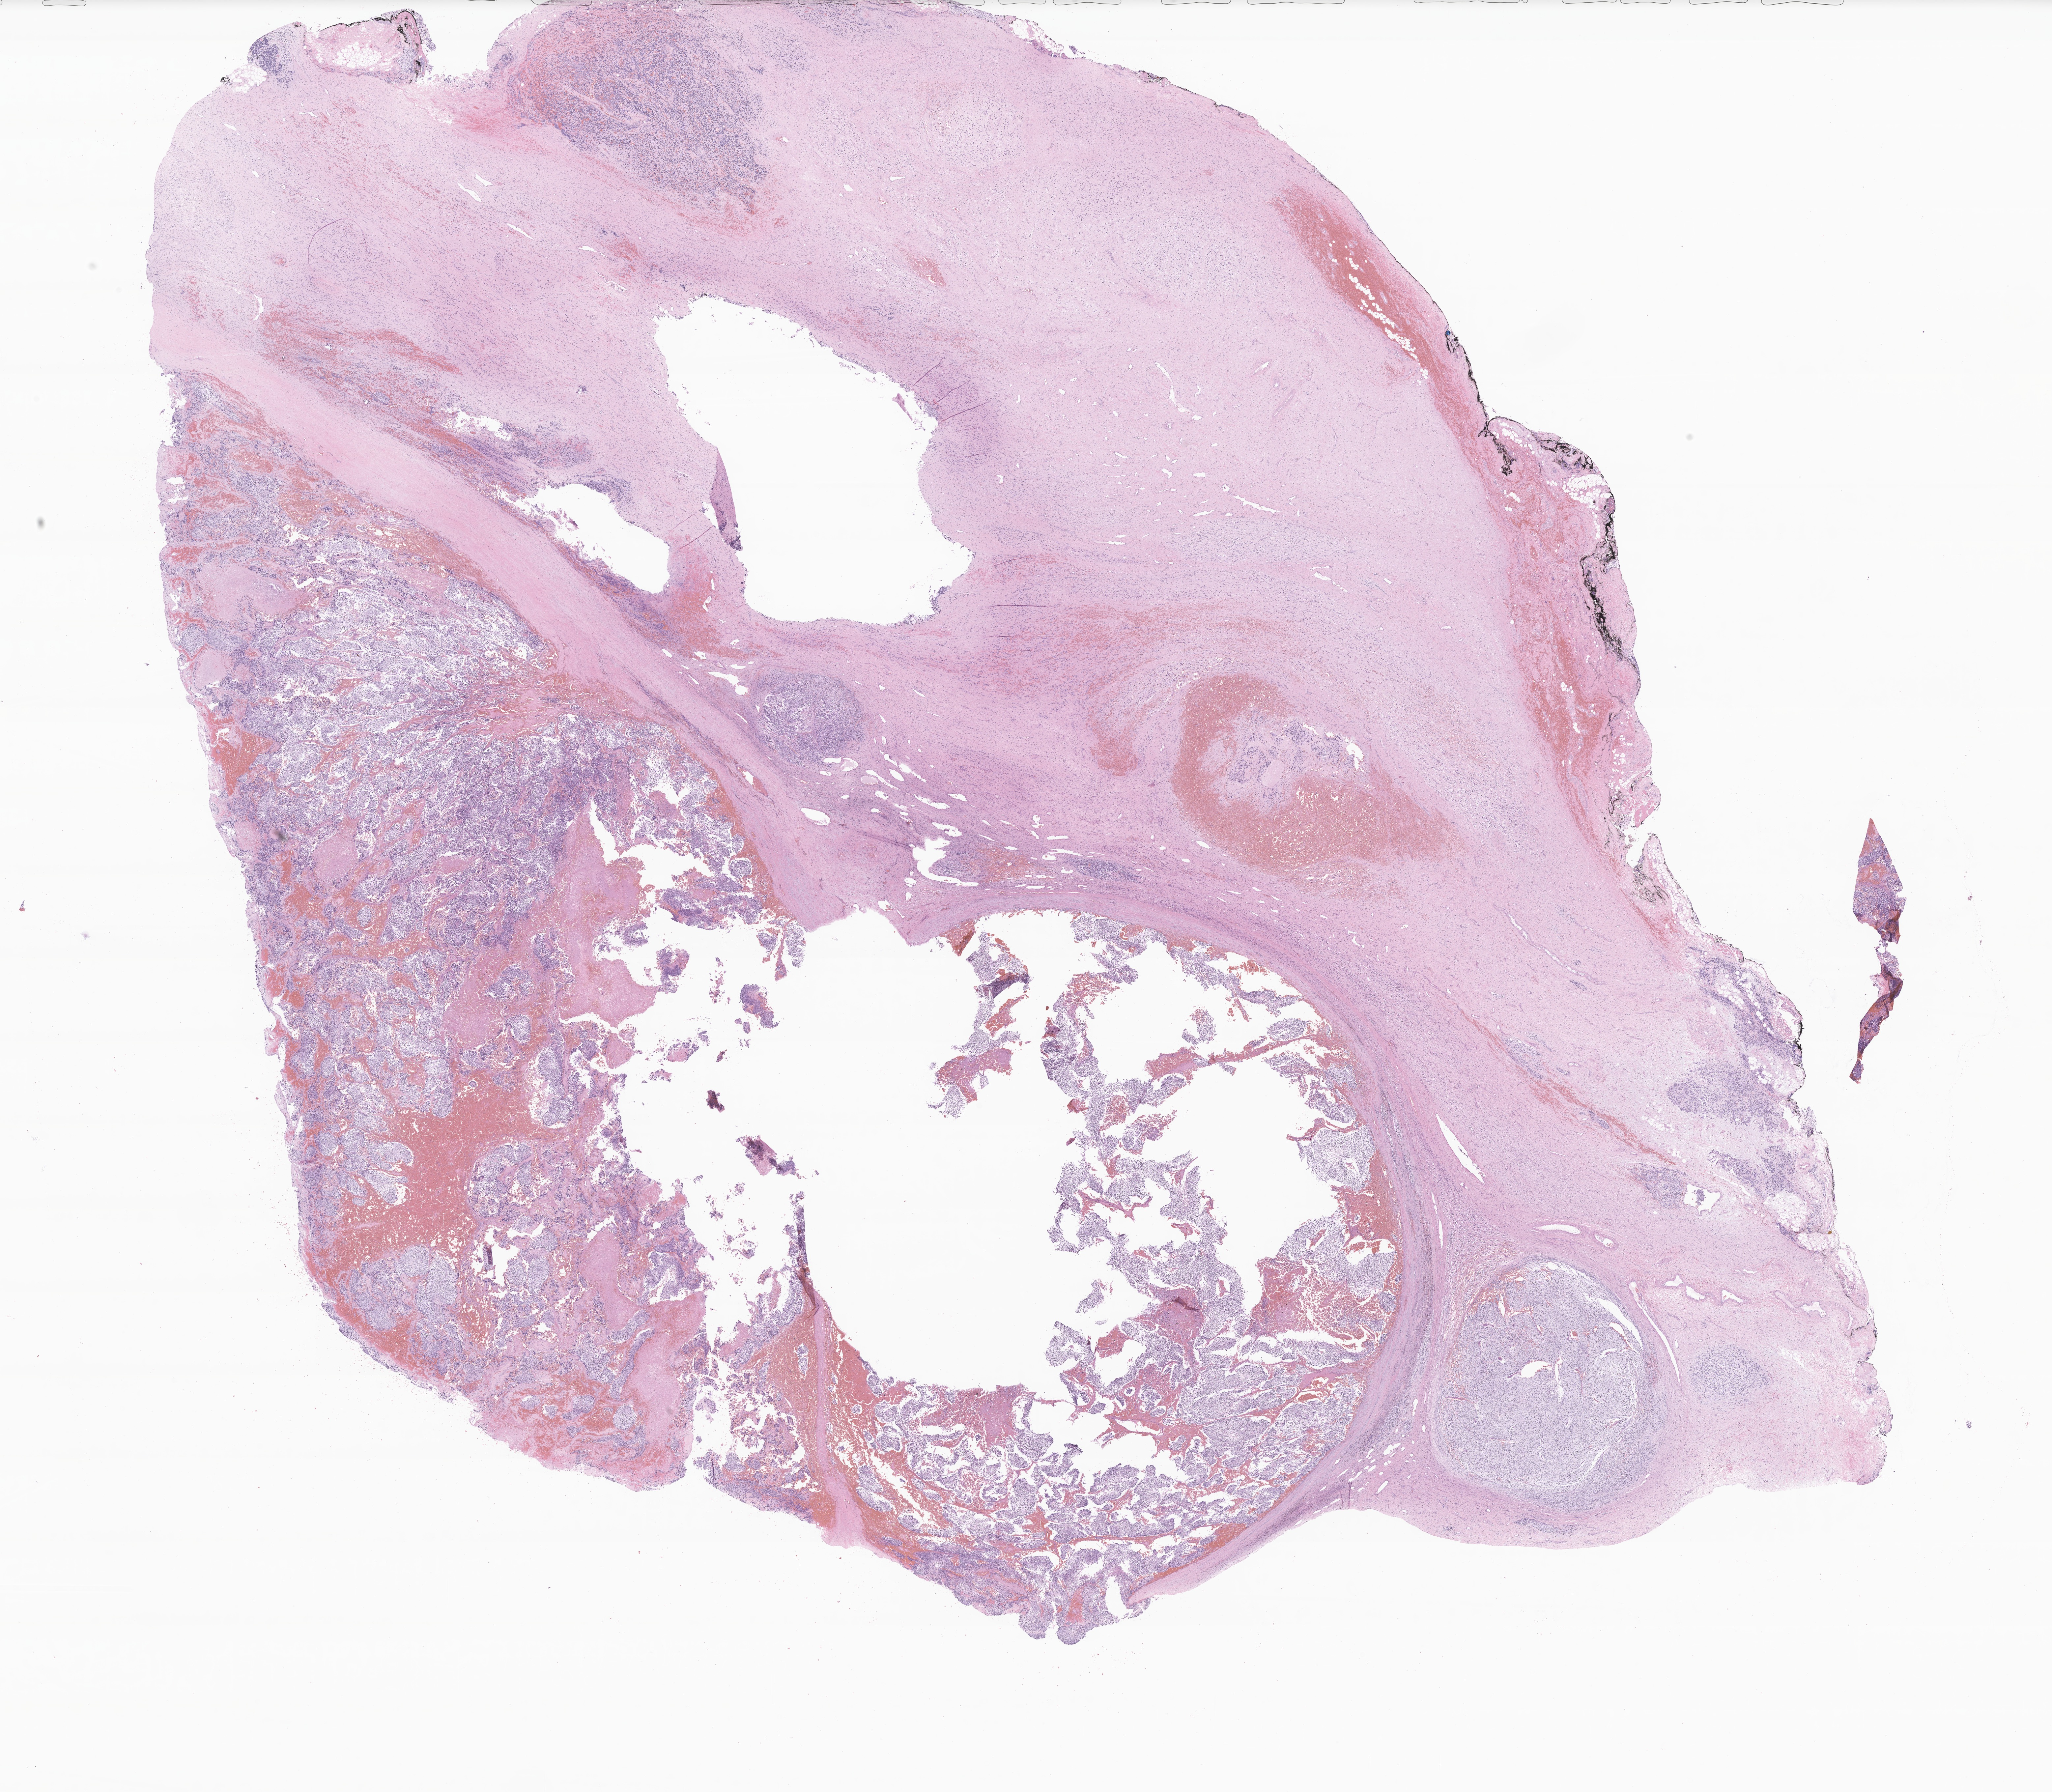
Hematoxylin and eosin (H&E) whole-slide image of tumor tissue from the posterior mediastinum, whole scanned area (about 26.3 x 22.9 mm) shown as a low-resolution overview; FFPE section. Male patient, age 113 months.
• diagnosis (ICD-O-3 morphology term): Neuroblastoma, NOS